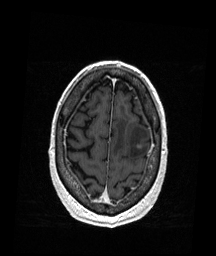
Brain MRI from a brain-tumour surgery series, one axial slice; position 42 of 176 along the scan axis; T1-weighted post-contrast; 1 mm slice thickness; 216 × 256 image matrix, field of view 211 × 250 mm. Case-level facts recorded for this patient, not image findings: histopathology: Metastatic Melanoma.
Annotated regions visible in this slice (manually delineated by an expert):
- tumour: box from (x=138, y=145) to (x=141, y=149) px